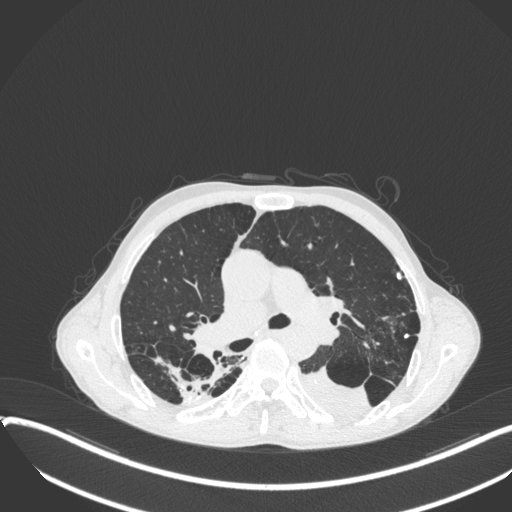
Chest CT, one axial slice. Reconstruction kernel B31f. Lung window (W 1500 / L -600 HU). 1 mm slice thickness. 512 × 512 image matrix, field of view 400 × 400 mm. Male patient, age 57 years. Case-level facts recorded for this patient, not image findings: clinical TNM (as recorded): T4 N0 M0.
Structures marked on this image (rectangle marked by the reading radiologist):
- lung tumour (recorded histology: squamous cell carcinoma): bounding box <295,357,373,418> (left, top, right, bottom; pixels)